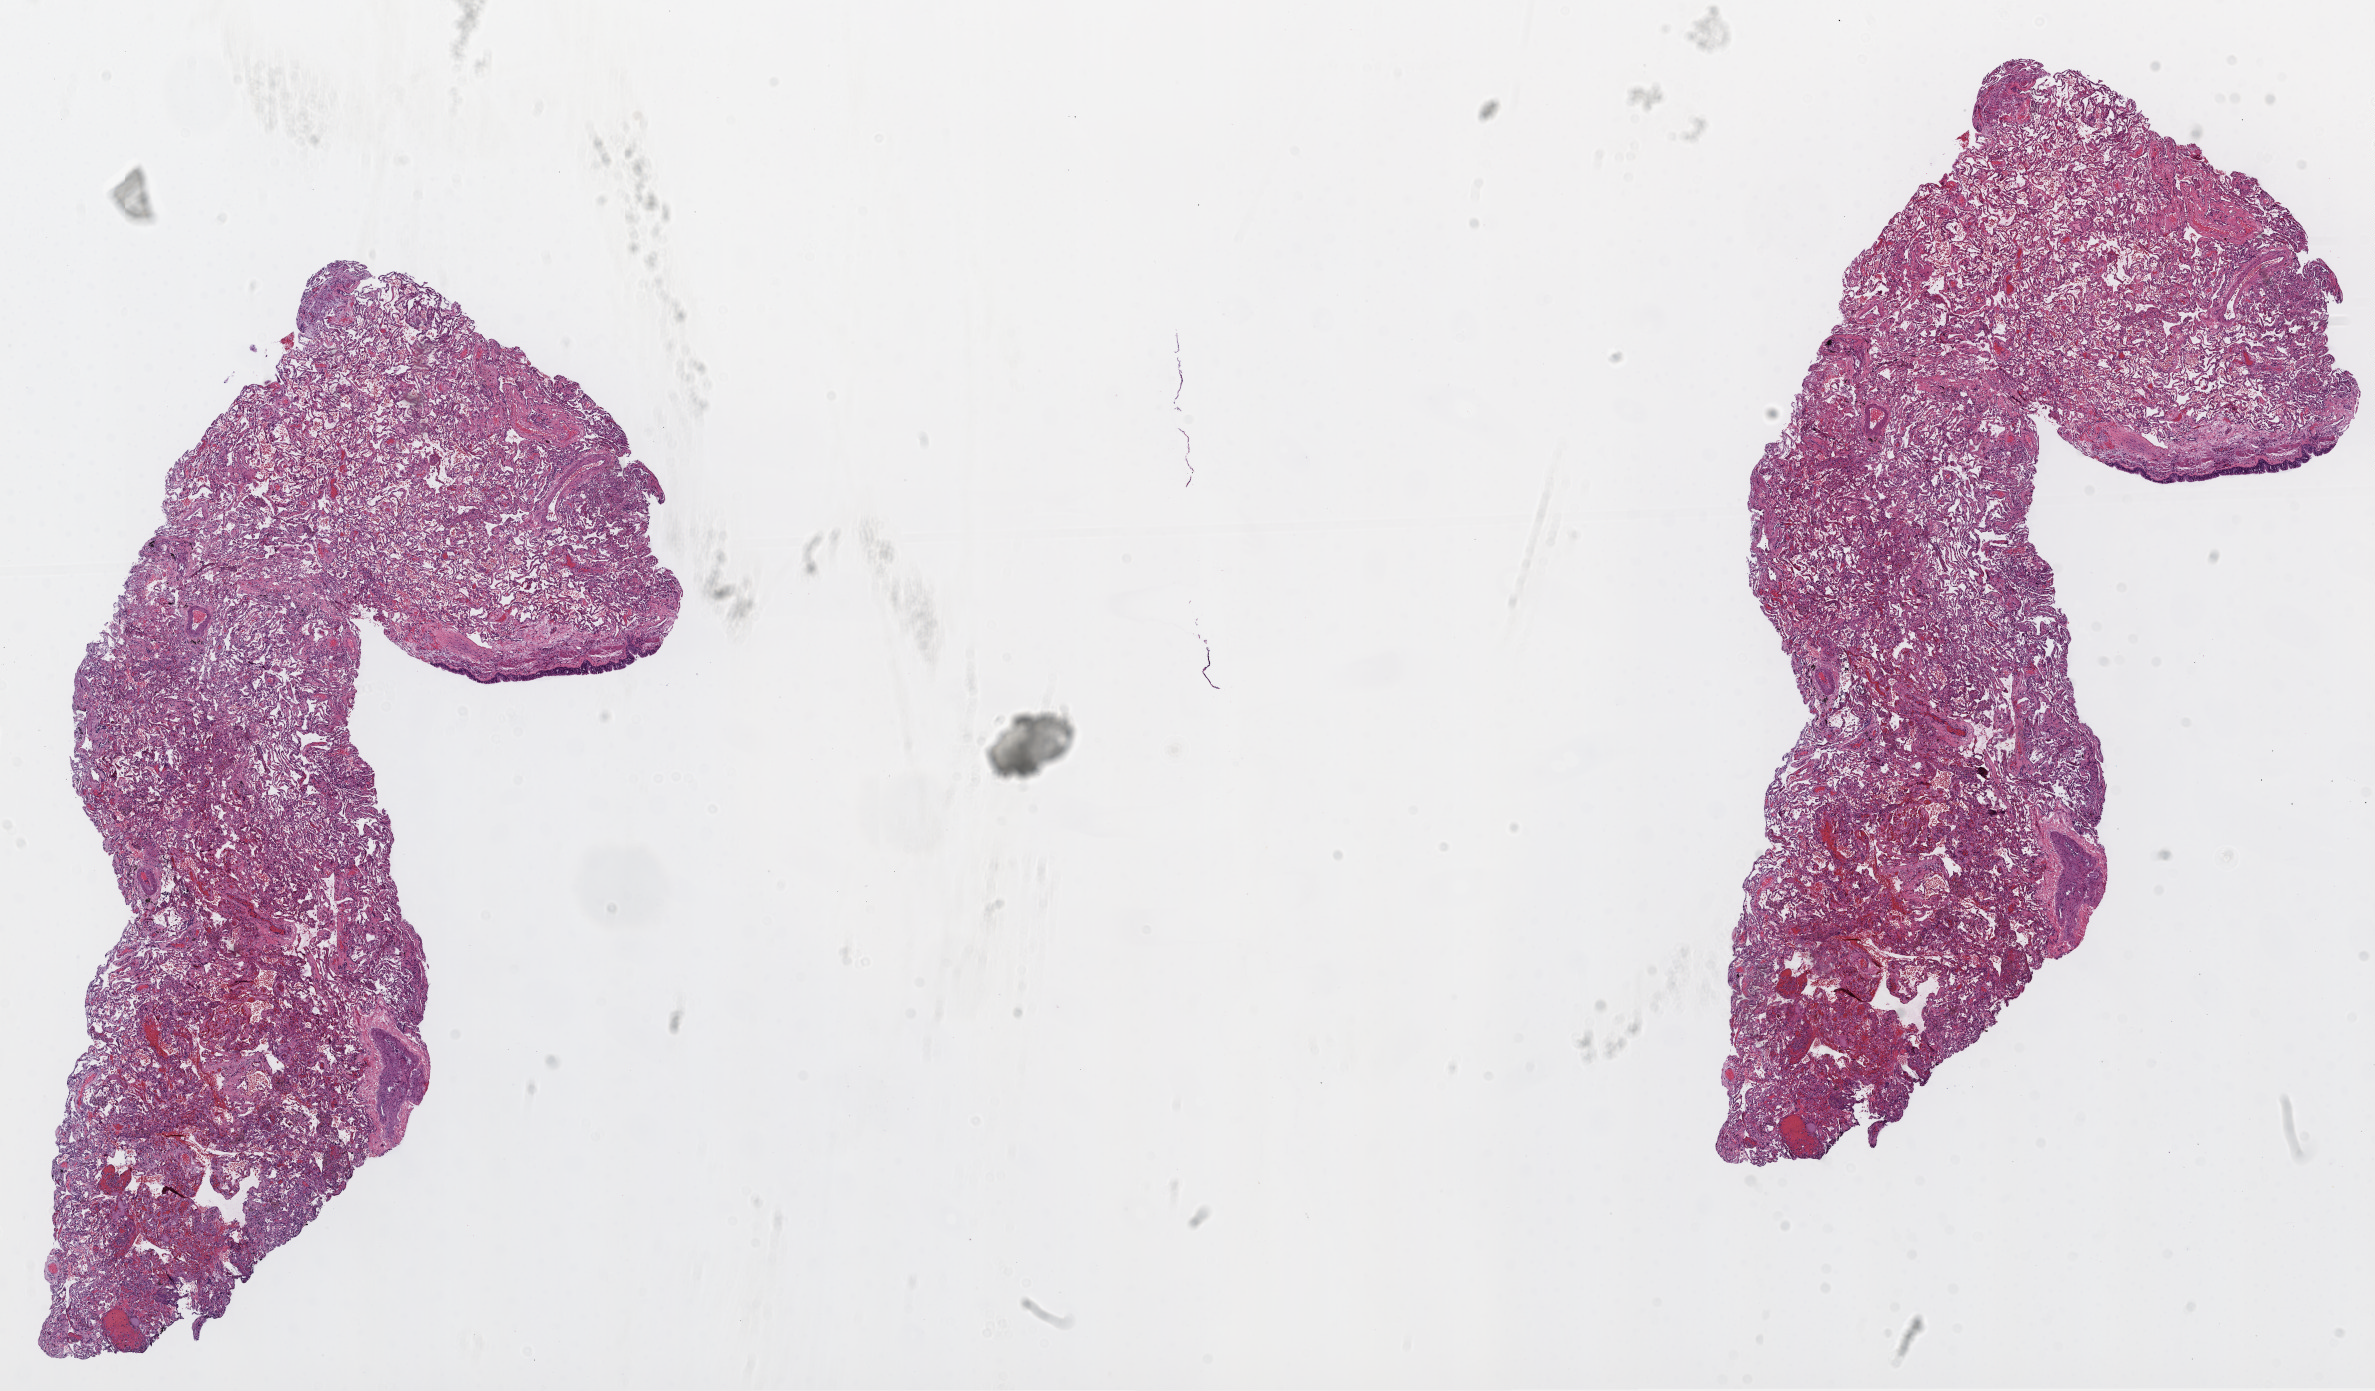
Whole-slide histology image, H&E, whole scanned area (about 19.1 x 11.2 mm) shown as a low-resolution overview; frozen section; solid tissue normal (non-tumour tissue) sample from the lung. Patient: female, age at initial diagnosis 59 years.
• this section: solid tissue normal sample (biorepository sample class)
• patient diagnosis: Squamous cell carcinoma, NOS (upper lobe, lung)